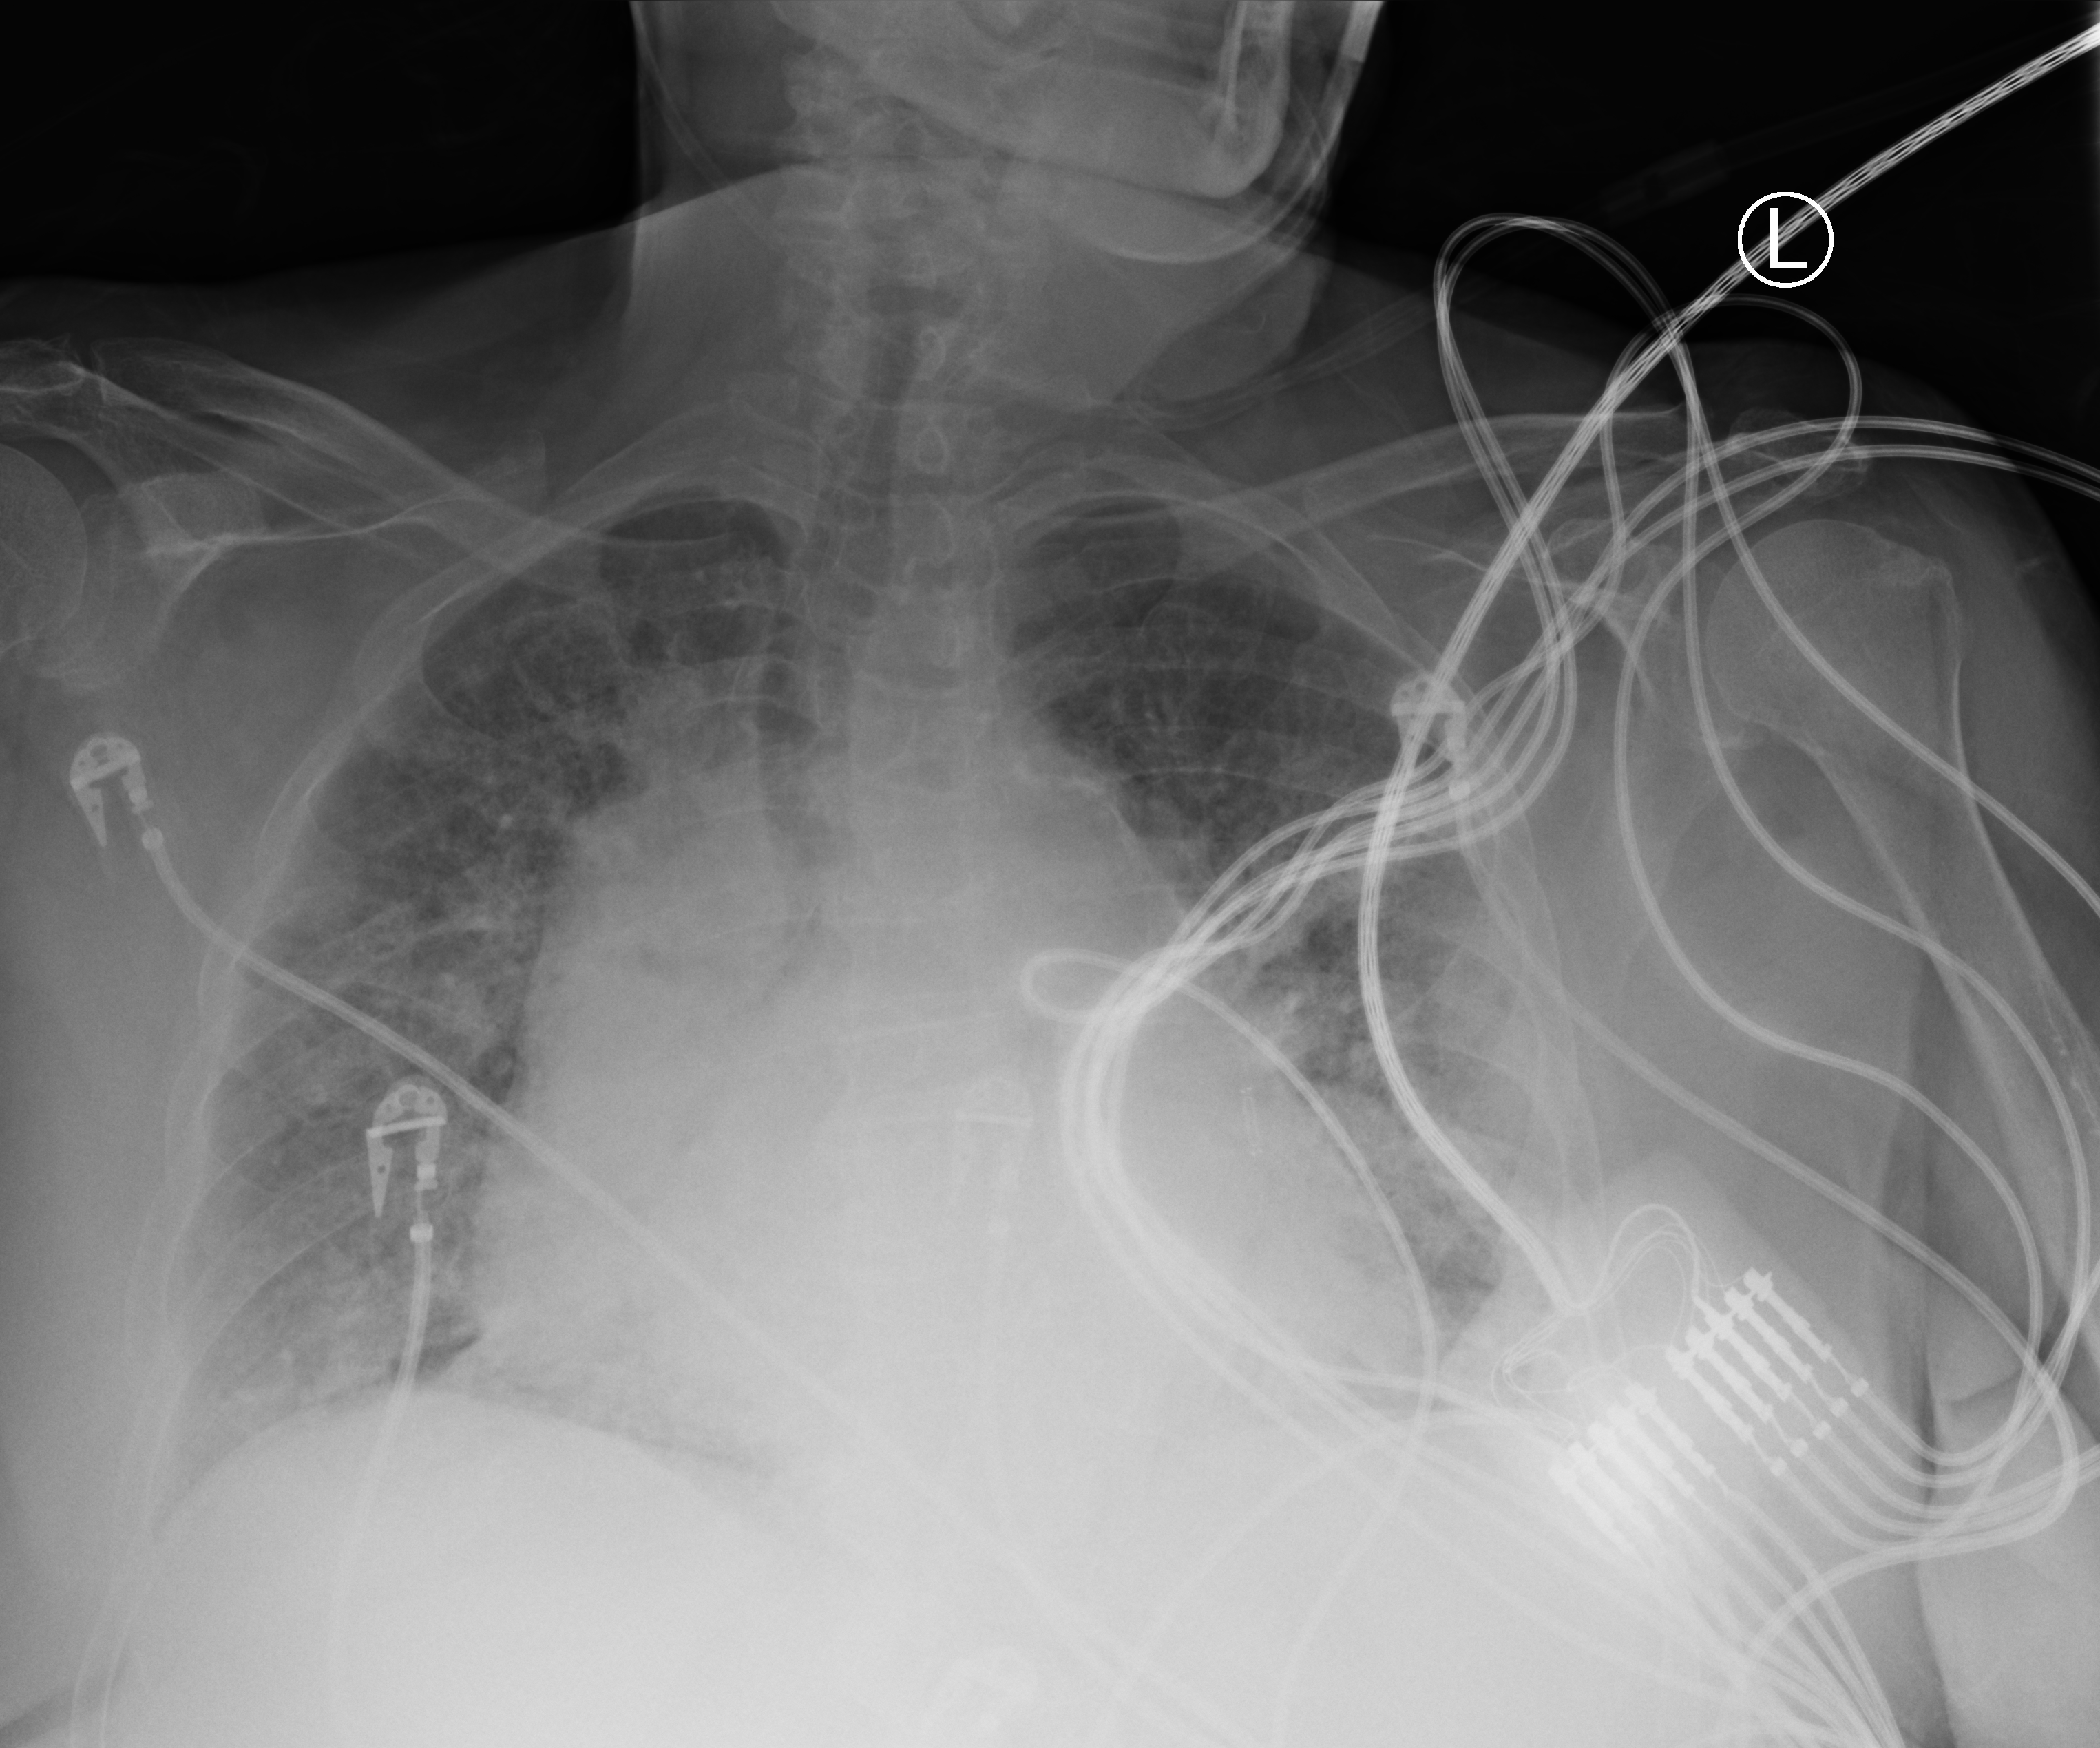
Chest X-ray (portable), anteroposterior (AP) projection. Female patient hospitalised with COVID-19, age 75–90 years.
Admission-level facts for this patient (not findings on this image; timing relative to this image not recorded): mechanically ventilated during this hospital stay: yes; admitted to intensive care during this hospital stay: yes.